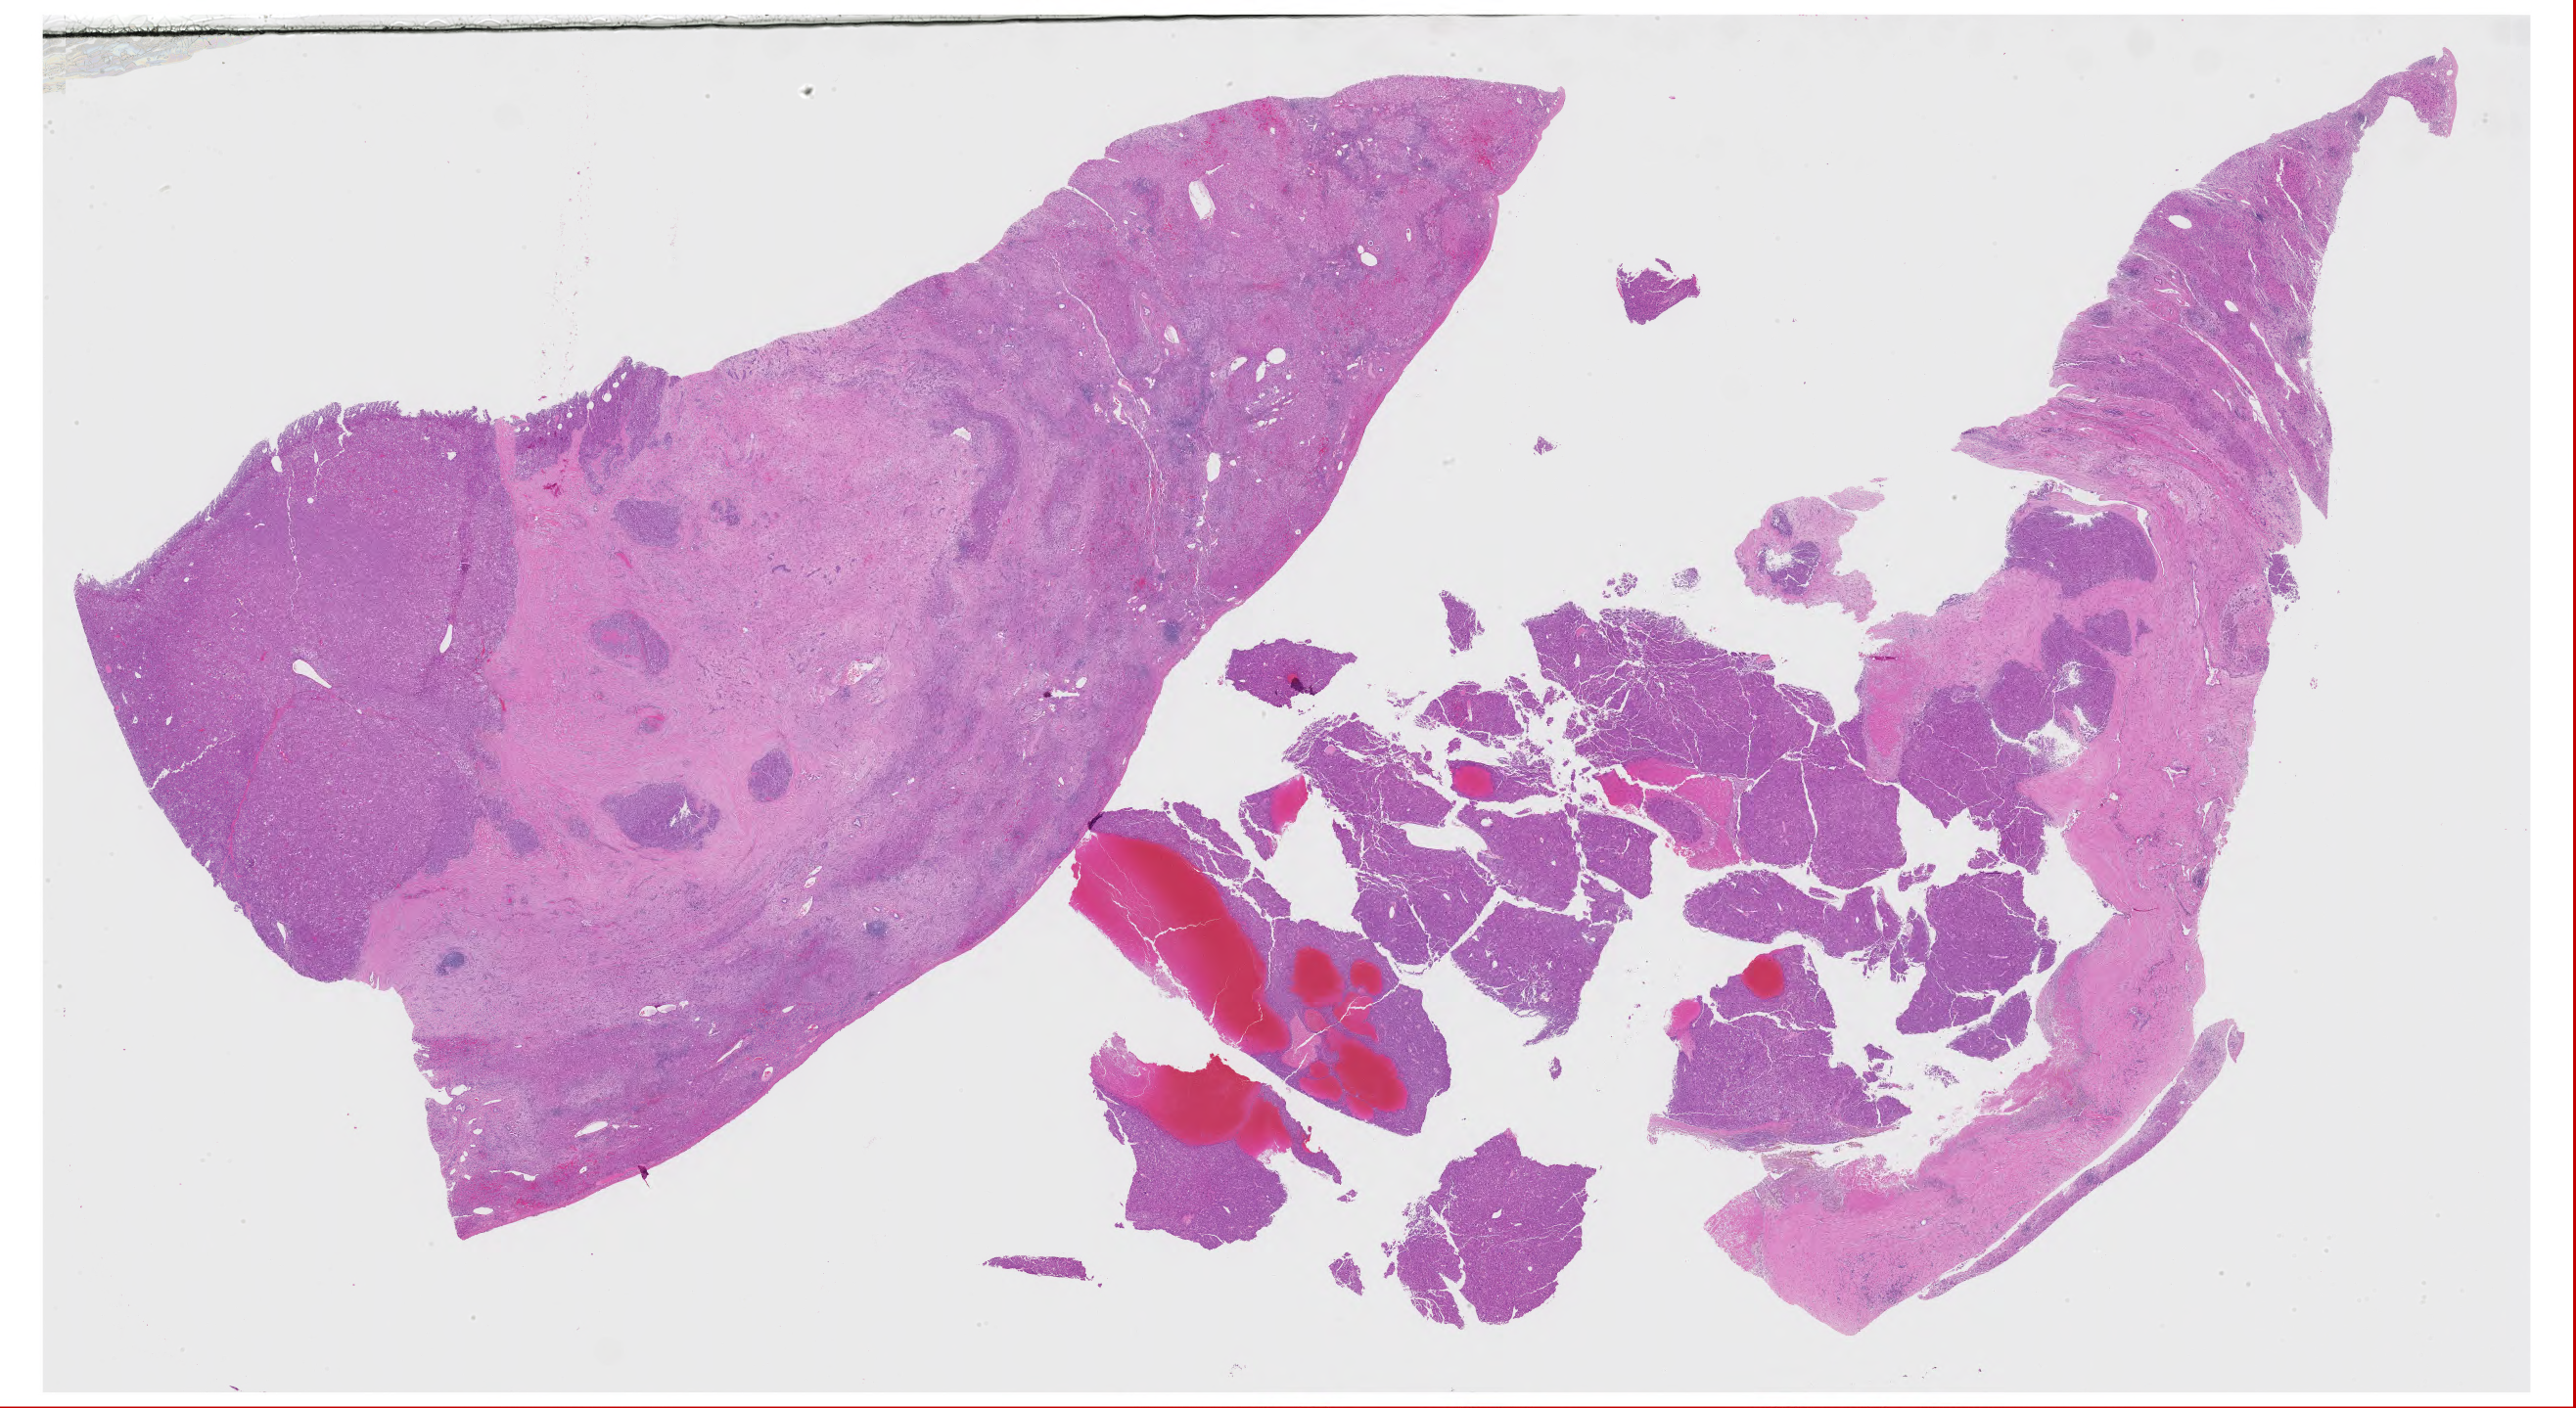
Digitized H&E tissue section (whole slide), shown as a low-resolution overview of the whole scanned area (about 42.1 x 23.0 mm, from a 20x scan); FFPE section; sample: primary tumour, liver. Female, age 72 years at initial diagnosis.
Pathologic diagnosis: Hepatocellular carcinoma, NOS.